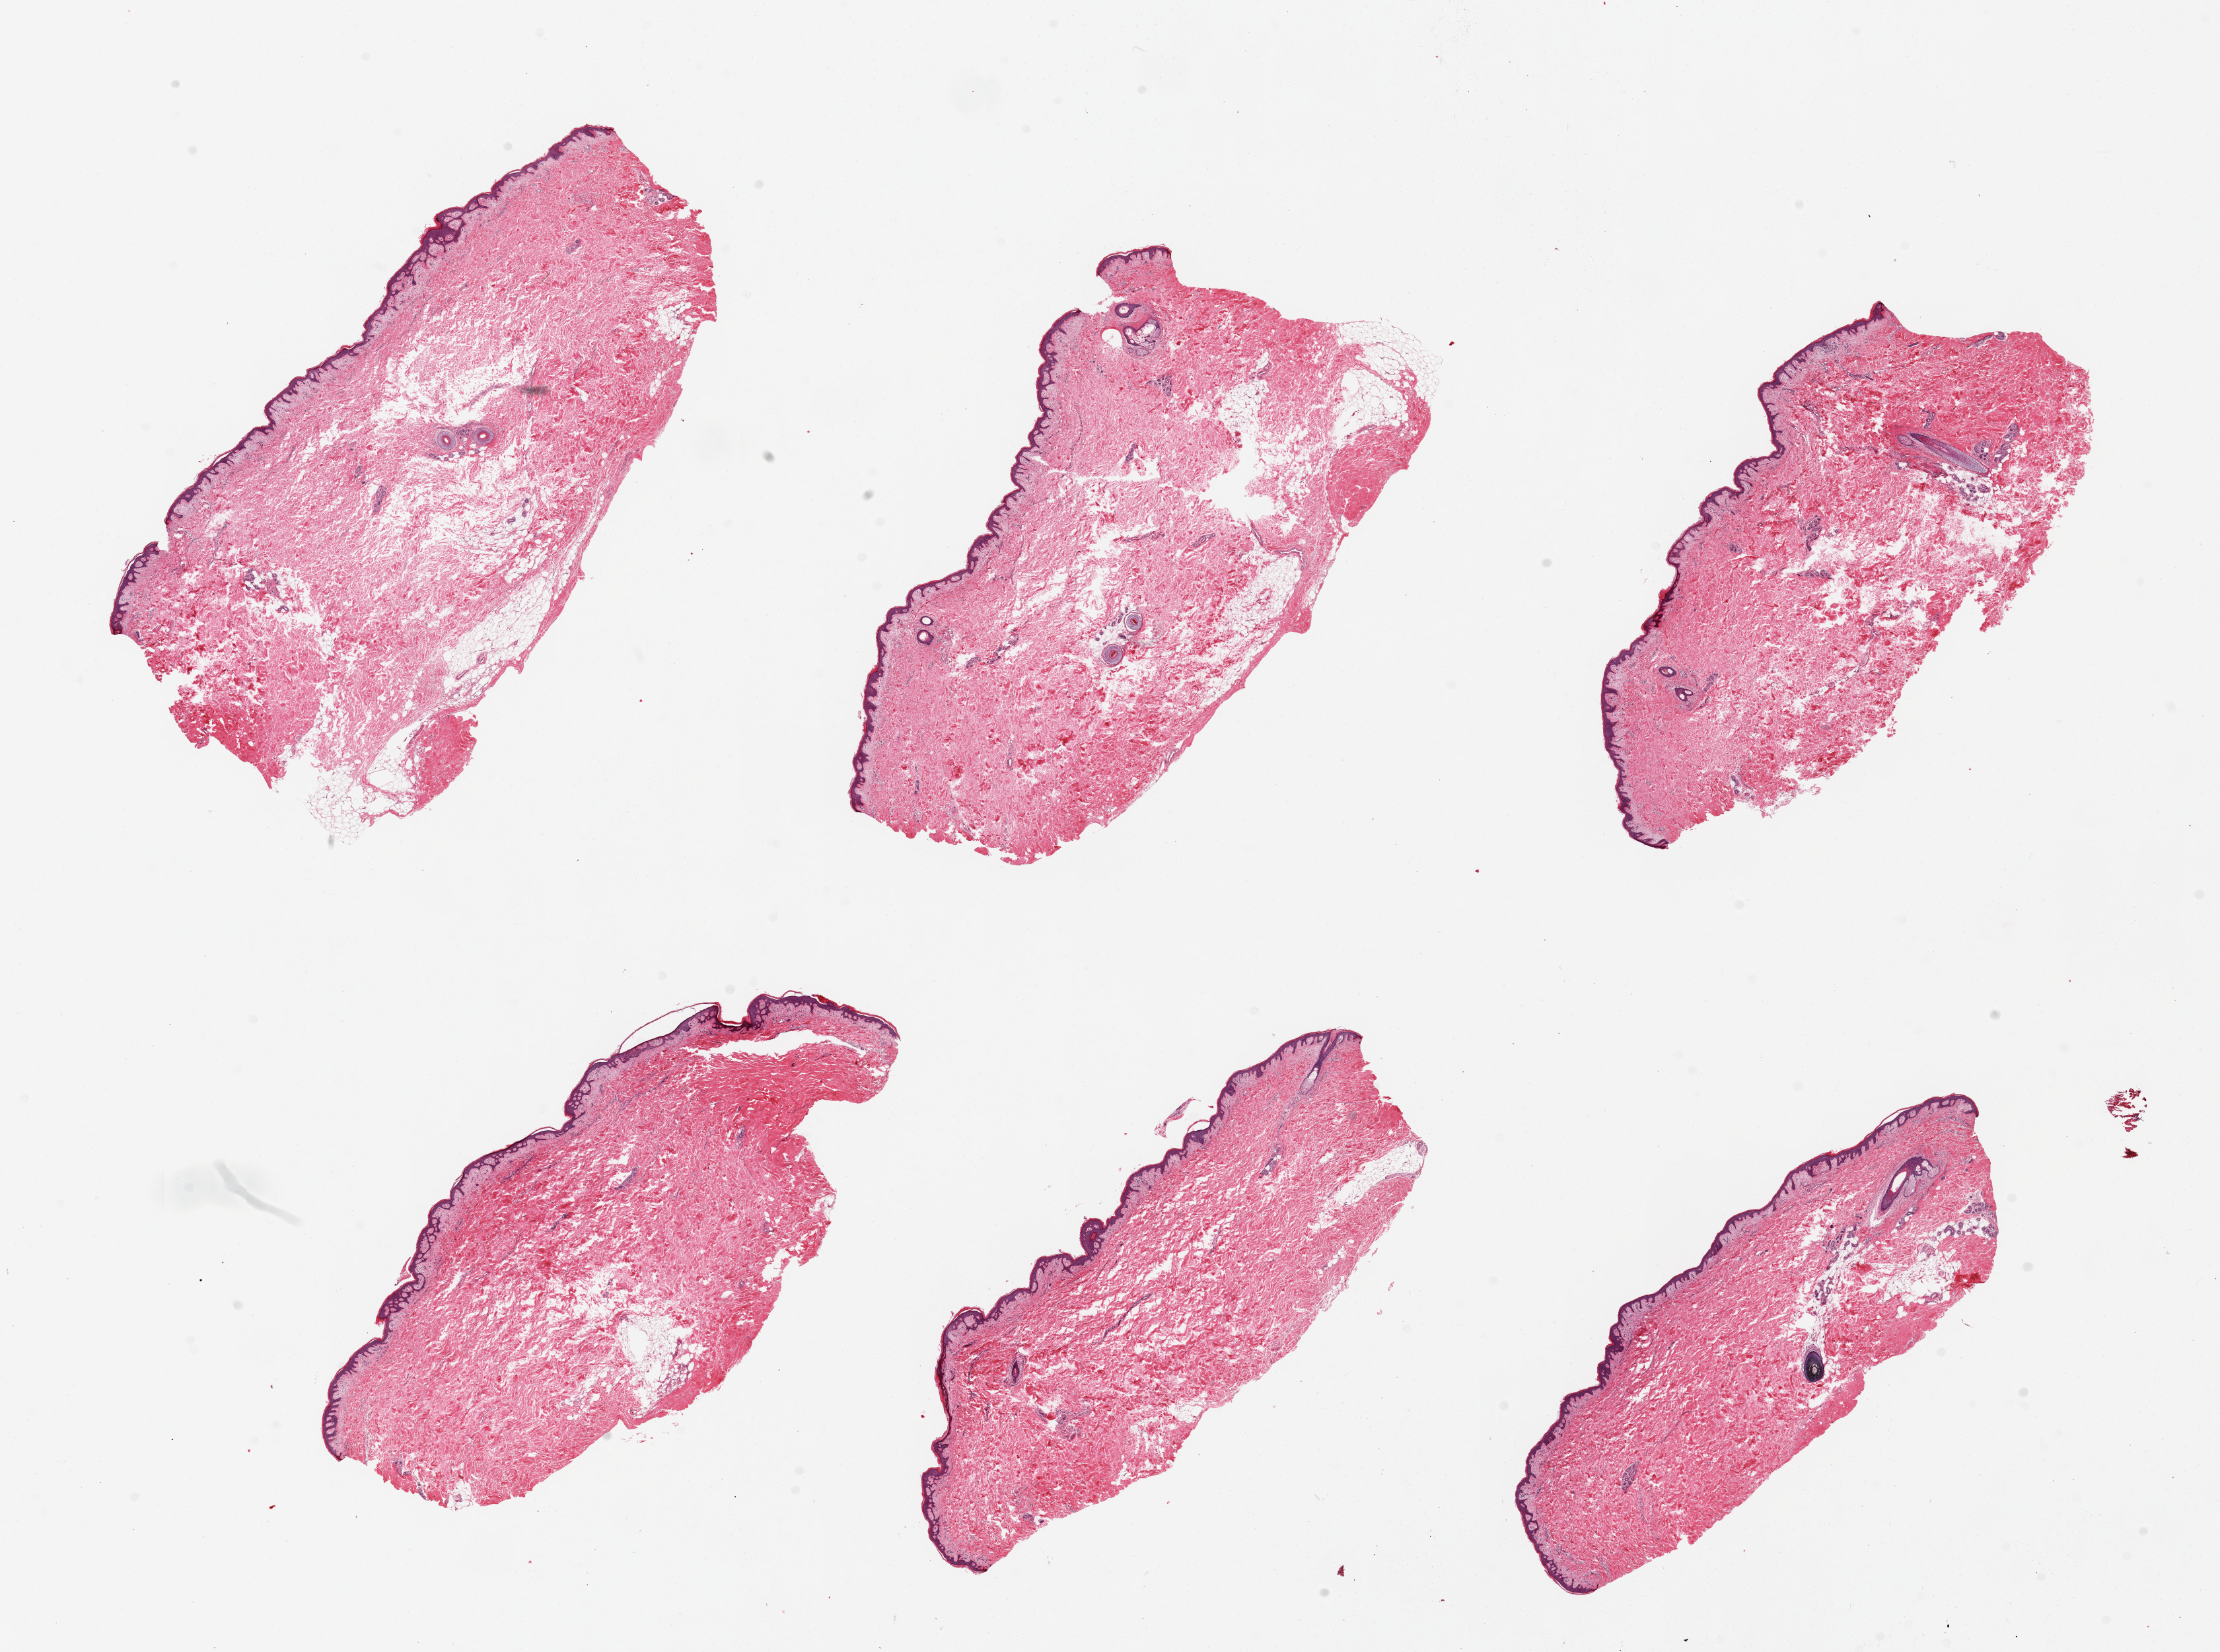
Digitized H&E-stained section, low-resolution overview of the scanned area, about 26.6 x 19.8 mm; PAXgene-fixed, paraffin-embedded tissue; target tissue: skin of suprapubic region; tissue donor sample. Donor: male.
* review note (as recorded): 6 pieces, from 8x3 to 9x4.5mm; squamous mucosa is 1-2% thickness